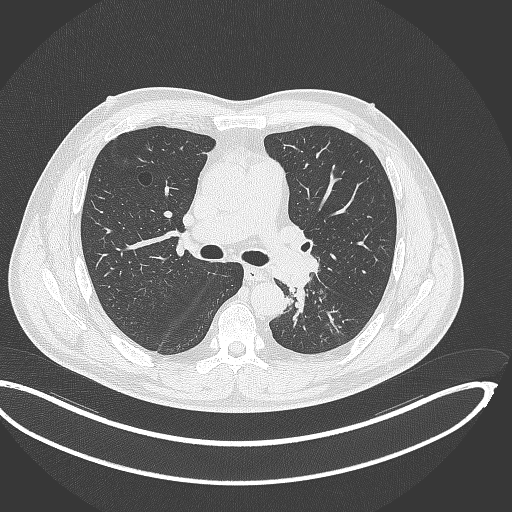
Chest CT, one axial slice. Position 215 of 362 along the scan axis. Reconstruction kernel B70f. 120 kVp. Lung window (W 1500 / L -600 HU). 1 mm slice thickness. 512 × 512 image matrix, field of view 442 × 442 mm. Patient: male, 50 years. From the clinical record (not read from this slice): clinical TNM (as recorded): T2a N3 M0.
Annotated regions visible in this slice (rectangle marked by the reading radiologist):
- lung tumour (recorded histology: squamous cell carcinoma): bounding box [x1, y1, x2, y2] px = [283, 269, 309, 325]